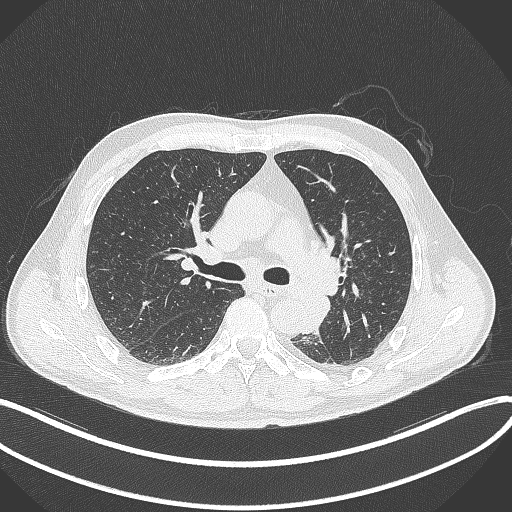
Chest CT, one axial slice; slice 214 of 329 in the series (ordered by position); reconstruction kernel B70f; lung window (W 1500 / L -600 HU); 1 mm slice thickness; 512 × 512 image matrix, field of view 400 × 400 mm. Patient: male, 59 years. Case-level facts recorded for this patient, not image findings: clinical TNM (as recorded): T2a N2 M0.
Structures marked on this image (rectangle marked by the reading radiologist):
- lung tumour (recorded histology: squamous cell carcinoma): bounding box <300,292,332,336> (left, top, right, bottom; pixels)